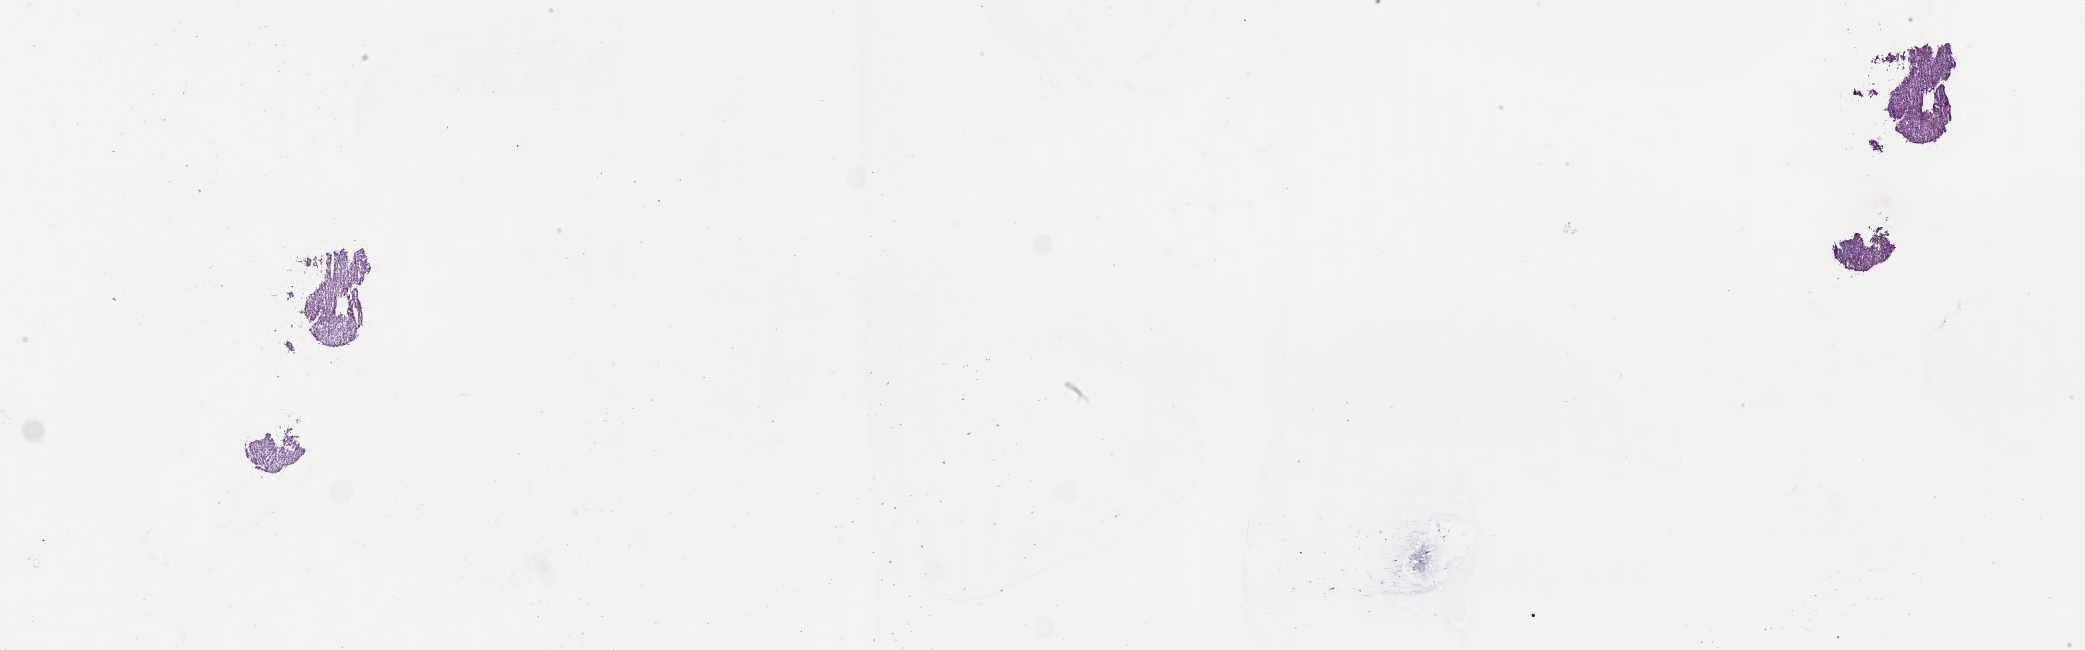
Digitized hematoxylin and eosin (H&E)-stained section of tumor tissue from the short bone of lower limb — low-resolution overview of the scanned area, about 33.7 x 10.5 mm. Frozen section (OCT-embedded). Female patient, age 162 months (13 years 6 months).
Diagnosis (ICD-O-3 morphology term): Undifferentiated sarcoma.